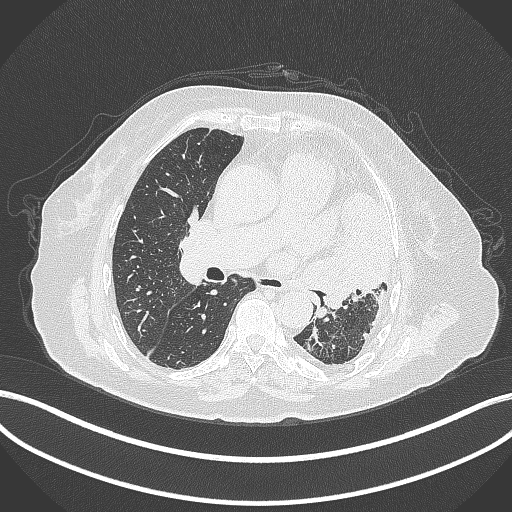
Chest CT, one axial slice. Slice 202 of 399 in the series (ordered by position). Reconstruction kernel B70f. Lung window (W 1500 / L -600 HU). 1 mm slice thickness. 512 × 512 image matrix, field of view 400 × 400 mm. Female patient, age 75 years. From the clinical record (not read from this slice): clinical TNM (as recorded): T3 N3 M1.
Outlined on this slice (rectangle marked by the reading radiologist):
- lung tumour (recorded histology: adenocarcinoma): bounding box <298,190,393,314> (left, top, right, bottom; pixels)